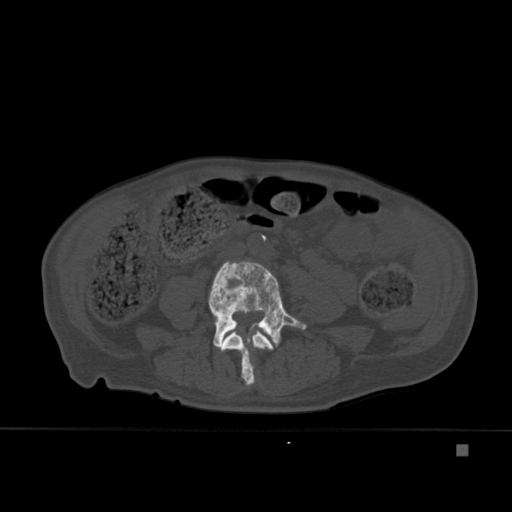
CT including the spine, one axial slice. Position 129 of 451 along the scan axis. Bone window (W 1800 / L 400 HU). 1.5 mm slice thickness. 512 × 512 image matrix. Patient: male, 75 years. Case-level facts recorded for this patient, not image findings: primary cancer: prostate.
Structures marked on this image (semi-automatically segmented with operator editing):
- L3 vertebra: box from (x=219, y=328) to (x=274, y=386) px
- L4 vertebra: (x=208, y=261)–(x=307, y=381)